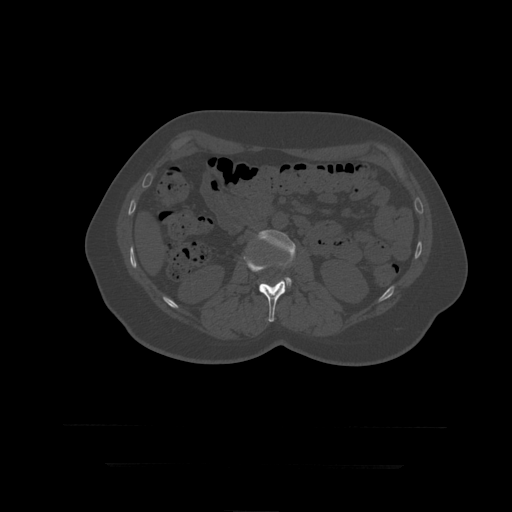
CT including the spine, one axial slice. Slice 140 of 399 in the series (ordered by position). Reconstruction kernel STANDARD. 120 kVp. Bone window (W 1800 / L 400 HU). 512 × 512 image matrix, field of view 450 × 450 mm. Patient age 41 years. From the clinical record (not read from this slice): primary cancer: breast.
Outlined on this slice (semi-automatically segmented with operator editing):
- L2 vertebra: box from (x=244, y=256) to (x=286, y=322) px
- L3 vertebra: (x=258, y=230)–(x=296, y=288)